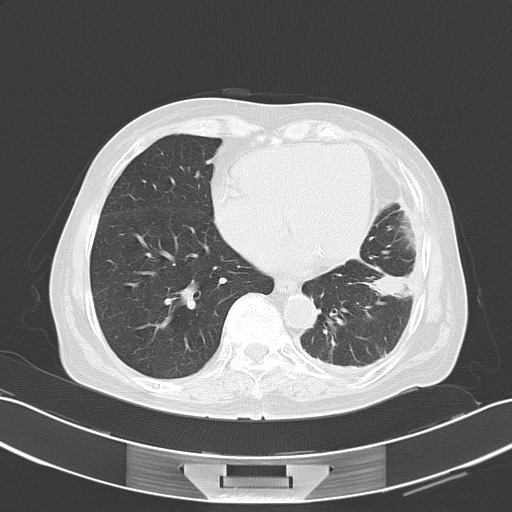
Chest CT, one axial slice. Slice 22 of 60 in the series (ordered by position). Reconstruction kernel B70f. 120 kVp. Lung window (W 1500 / L -600 HU). 5 mm slice thickness. 512 × 512 image matrix. Patient: female, 82 years. From the clinical record (not read from this slice): clinical TNM (as recorded): T1c N0 M1.
Annotated regions visible in this slice (bounding box drawn by a radiologist):
- lung tumour (recorded histology: adenocarcinoma): bounding box [x1, y1, x2, y2] px = [367, 264, 413, 301]